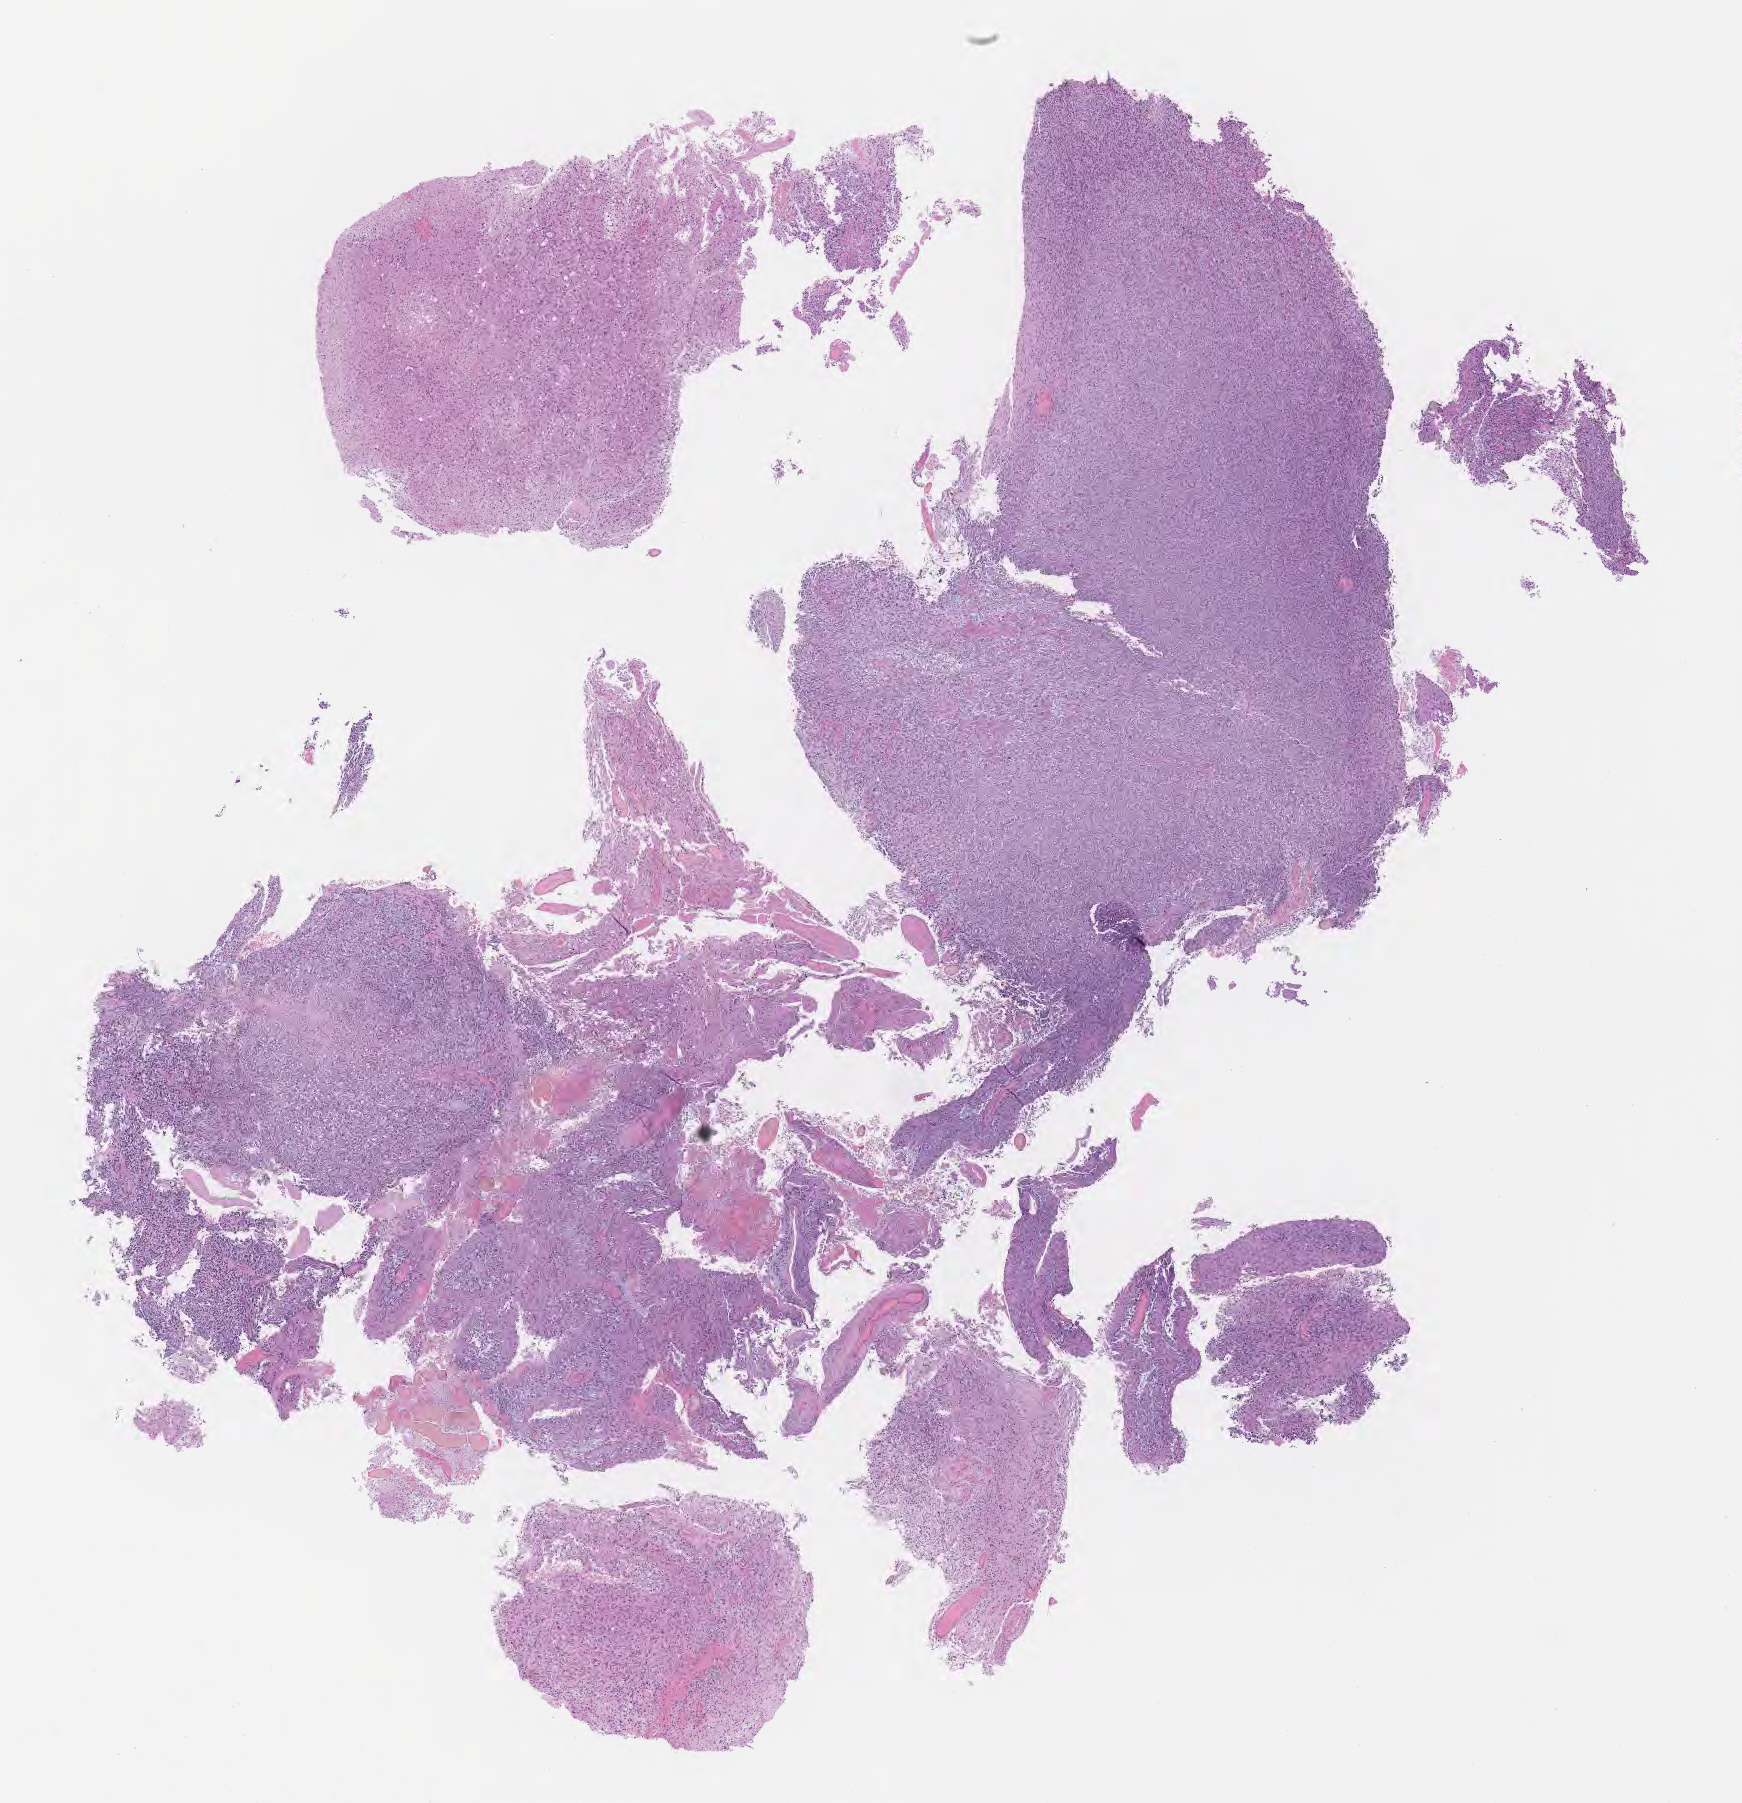
Whole-slide image, hematoxylin and eosin (H&E) stain, shown as a low-resolution overview of the whole scanned area (about 14.1 x 14.6 mm), formalin-fixed paraffin-embedded section, primary tumor, anatomic site: brain. Male, age 69 years at initial diagnosis. Slide review estimates, as recorded: tumor cells 87%, tumor nuclei 93%, stromal cells 5%, necrosis 2%, normal cells 6%. Infiltration values recorded for this section: lymphocyte infiltration 0%, monocyte infiltration 0%, neutrophil infiltration 0%.
Section: top of the tissue portion. Diagnosis: Glioblastoma, NOS.